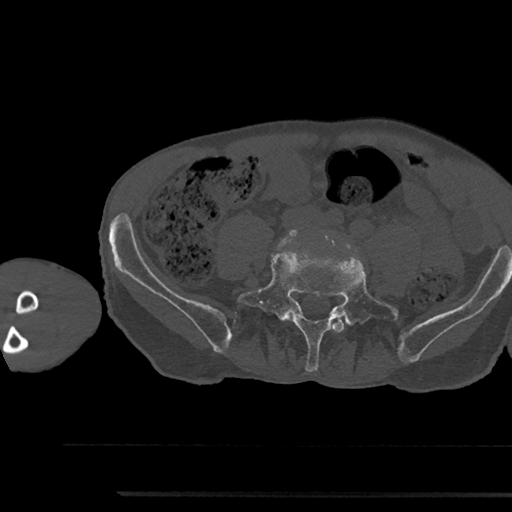
CT including the spine, one axial slice. Position 359 of 797 along the scan axis. 120 kVp. Bone window (W 1800 / L 400 HU). 0.5 mm slice thickness. 512 × 512 image matrix. Patient: male, 79 years. From the clinical record (not read from this slice): primary cancer: prostate.
Annotated regions visible in this slice (semi-automatically segmented with operator editing):
- L4 vertebra: bounding box [x1, y1, x2, y2] px = [332, 319, 345, 333]
- L5 vertebra: [238, 252, 399, 372]